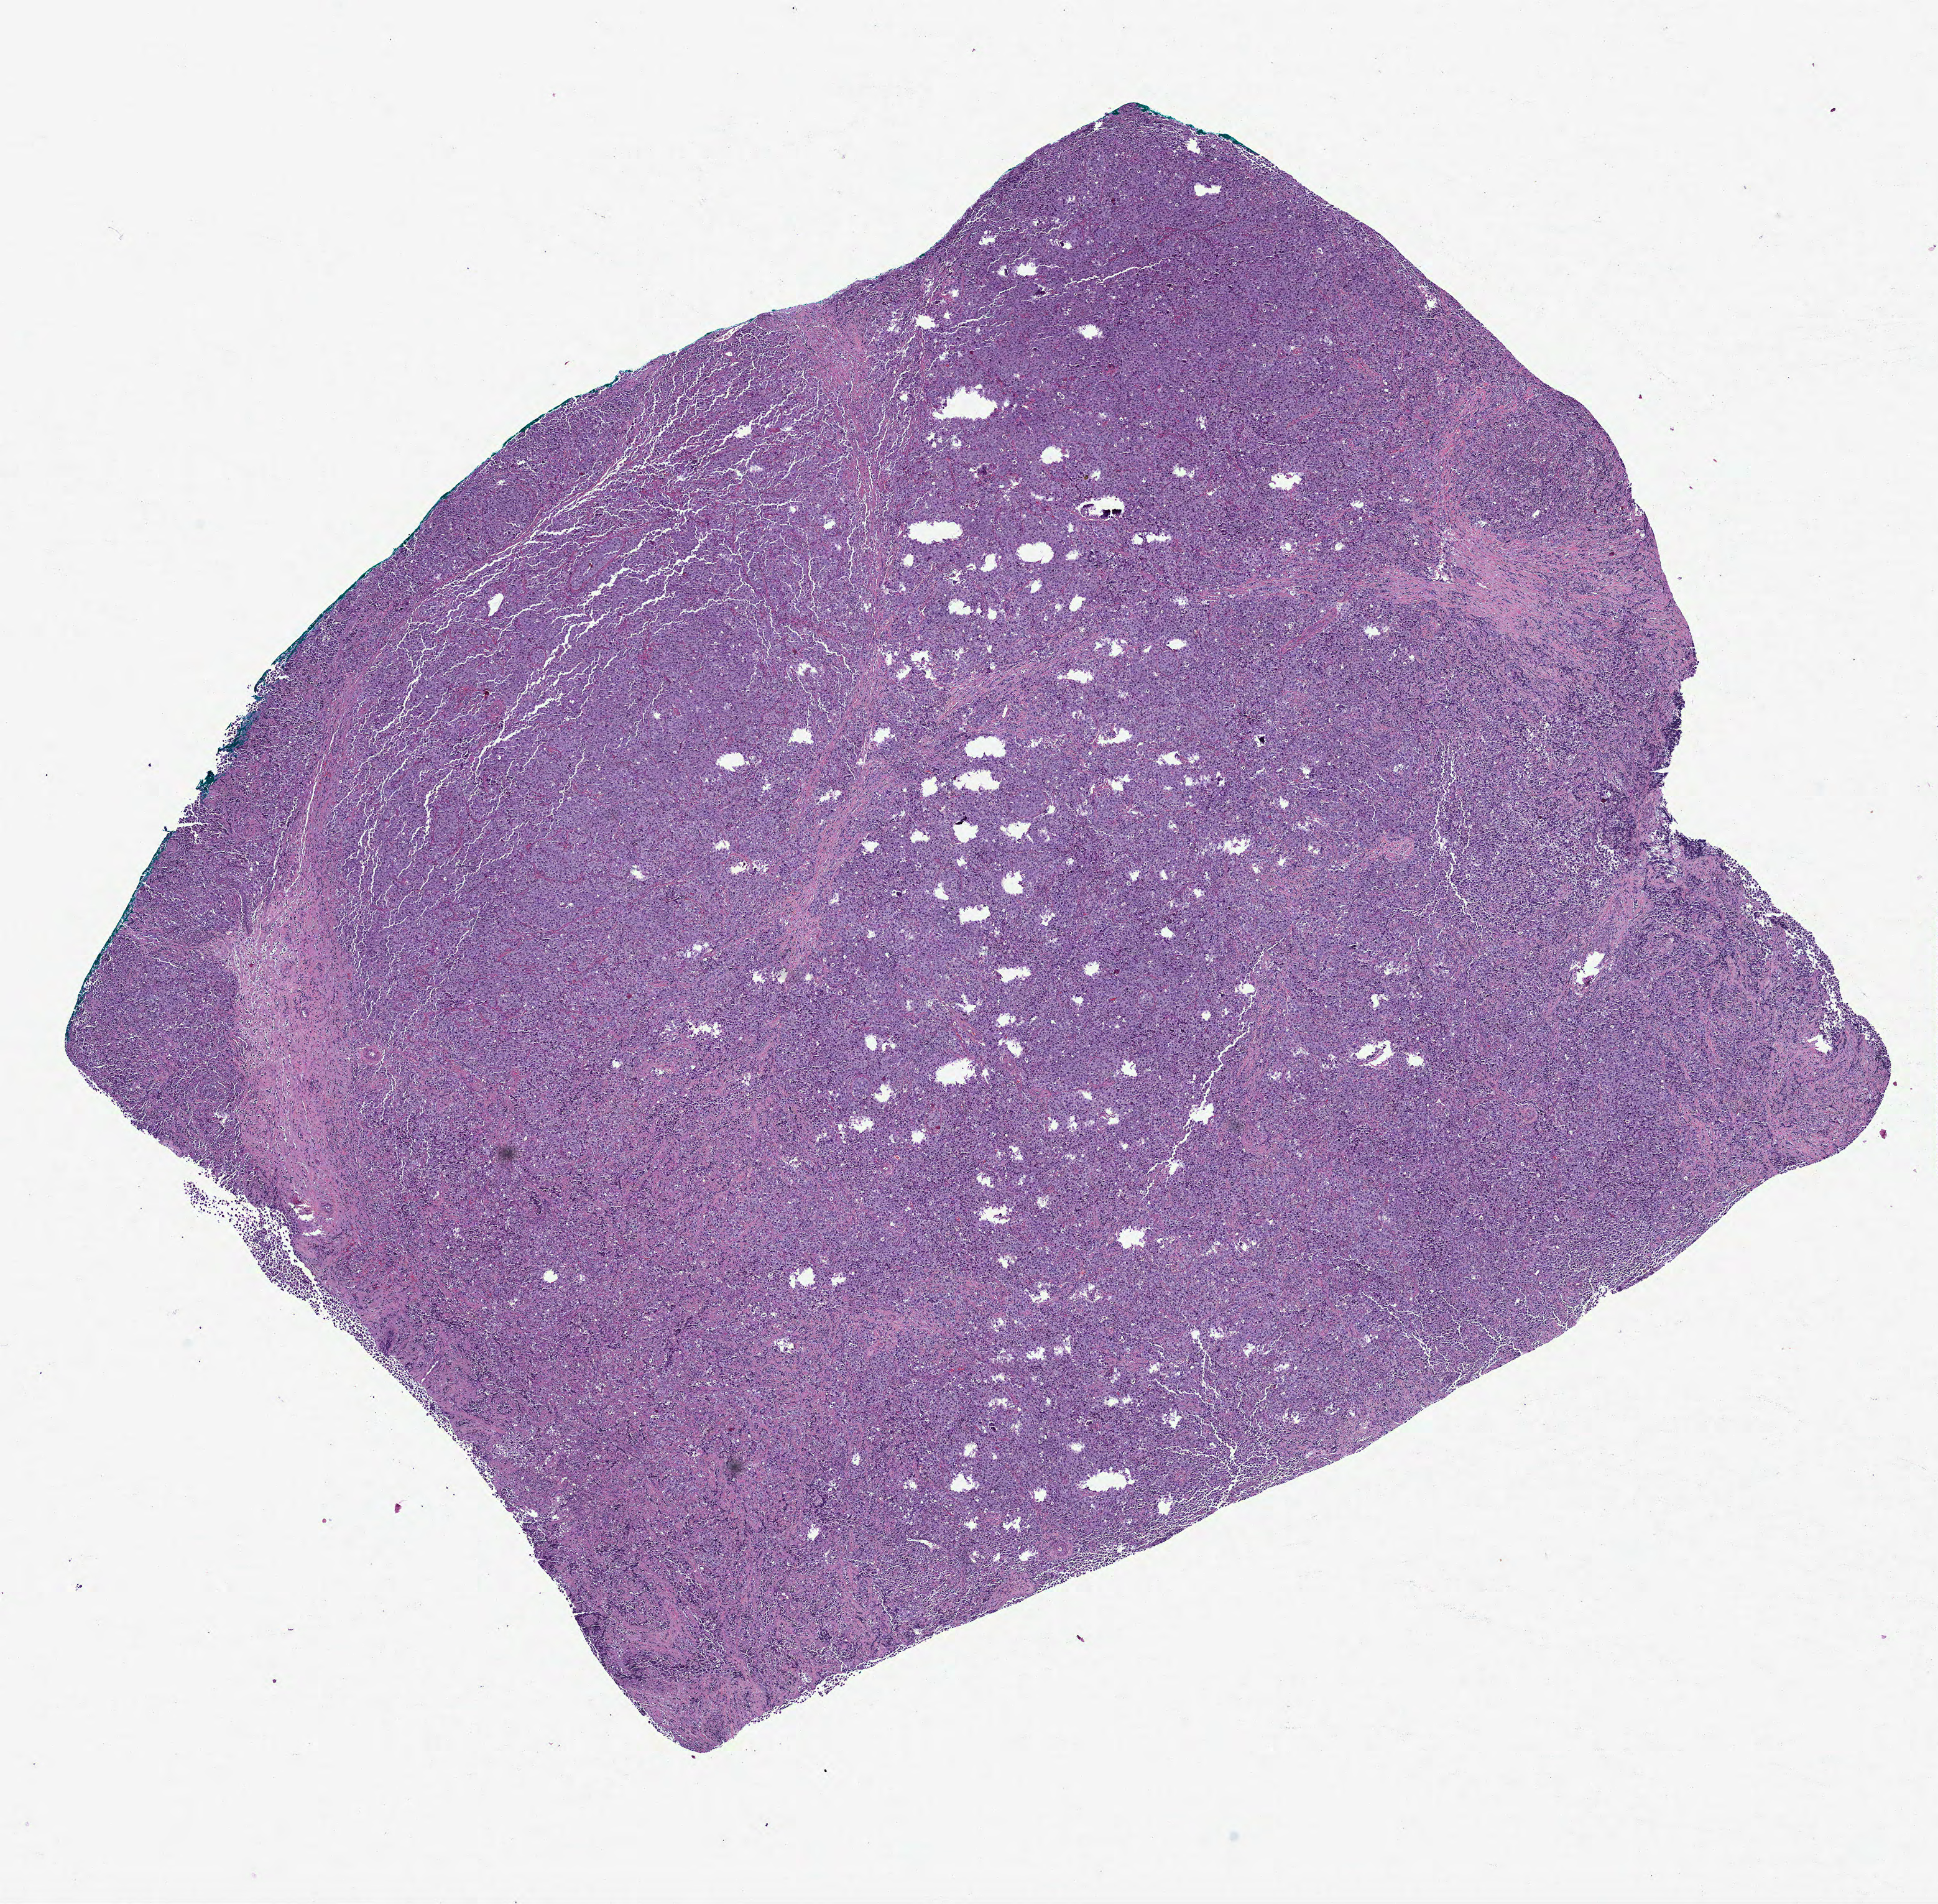
Whole-slide histology image, Hematoxylin and eosin (H&E) stained — low-resolution overview of the scanned area, about 12.6 x 12.3 mm; formalin-fixed paraffin-embedded (FFPE) diagnostic section; primary tumour sample from the testis. Male, age 27 years at initial diagnosis.
* pathologic diagnosis: Seminoma, NOS
* TNM: T2 NX
* AJCC pathologic stage: I
* laterality: right